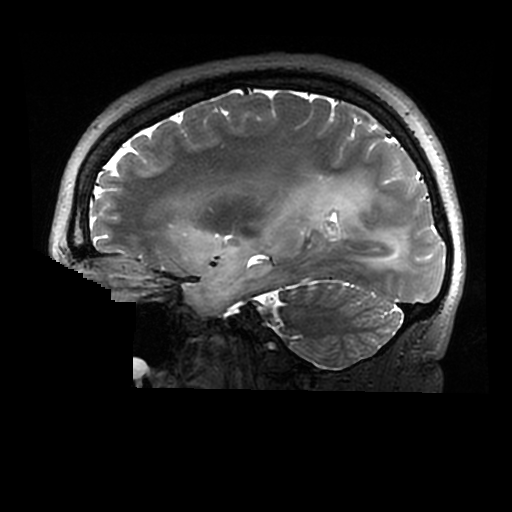
Brain MRI from a brain-tumour surgery series, one sagittal slice; position 189 of 320 along the scan axis; 0.6 mm slice thickness; 512 × 512 image matrix, field of view 240 × 240 mm. Case-level facts recorded for this patient, not image findings: histopathology: Astrocytoma; WHO grade: 2; IDH mutation: yes.
Structures marked on this image (outlined manually by an expert reader):
- tumour: bounding box <173,183,407,313> (left, top, right, bottom; pixels)